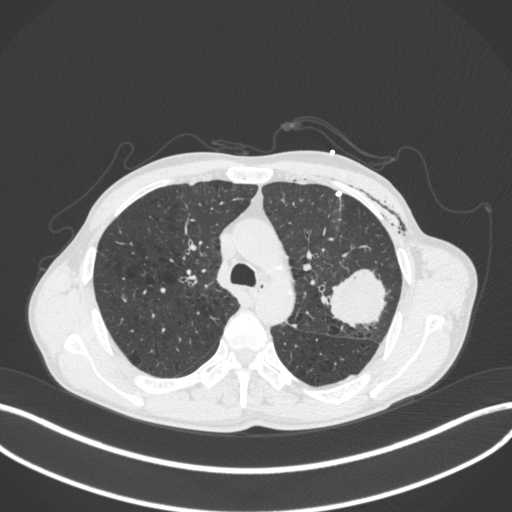
Chest CT, one axial slice. Position 279 of 416 along the scan axis. Lung window (W 1500 / L -600 HU). 1 mm slice thickness. 512 × 512 image matrix, field of view 400 × 400 mm. Male patient, age 58 years. From the clinical record (not read from this slice): clinical TNM (as recorded): T3 N0 M0.
Structures marked on this image (rectangle marked by the reading radiologist):
- lung tumour (recorded histology: adenocarcinoma): box from (x=316, y=264) to (x=392, y=327) px